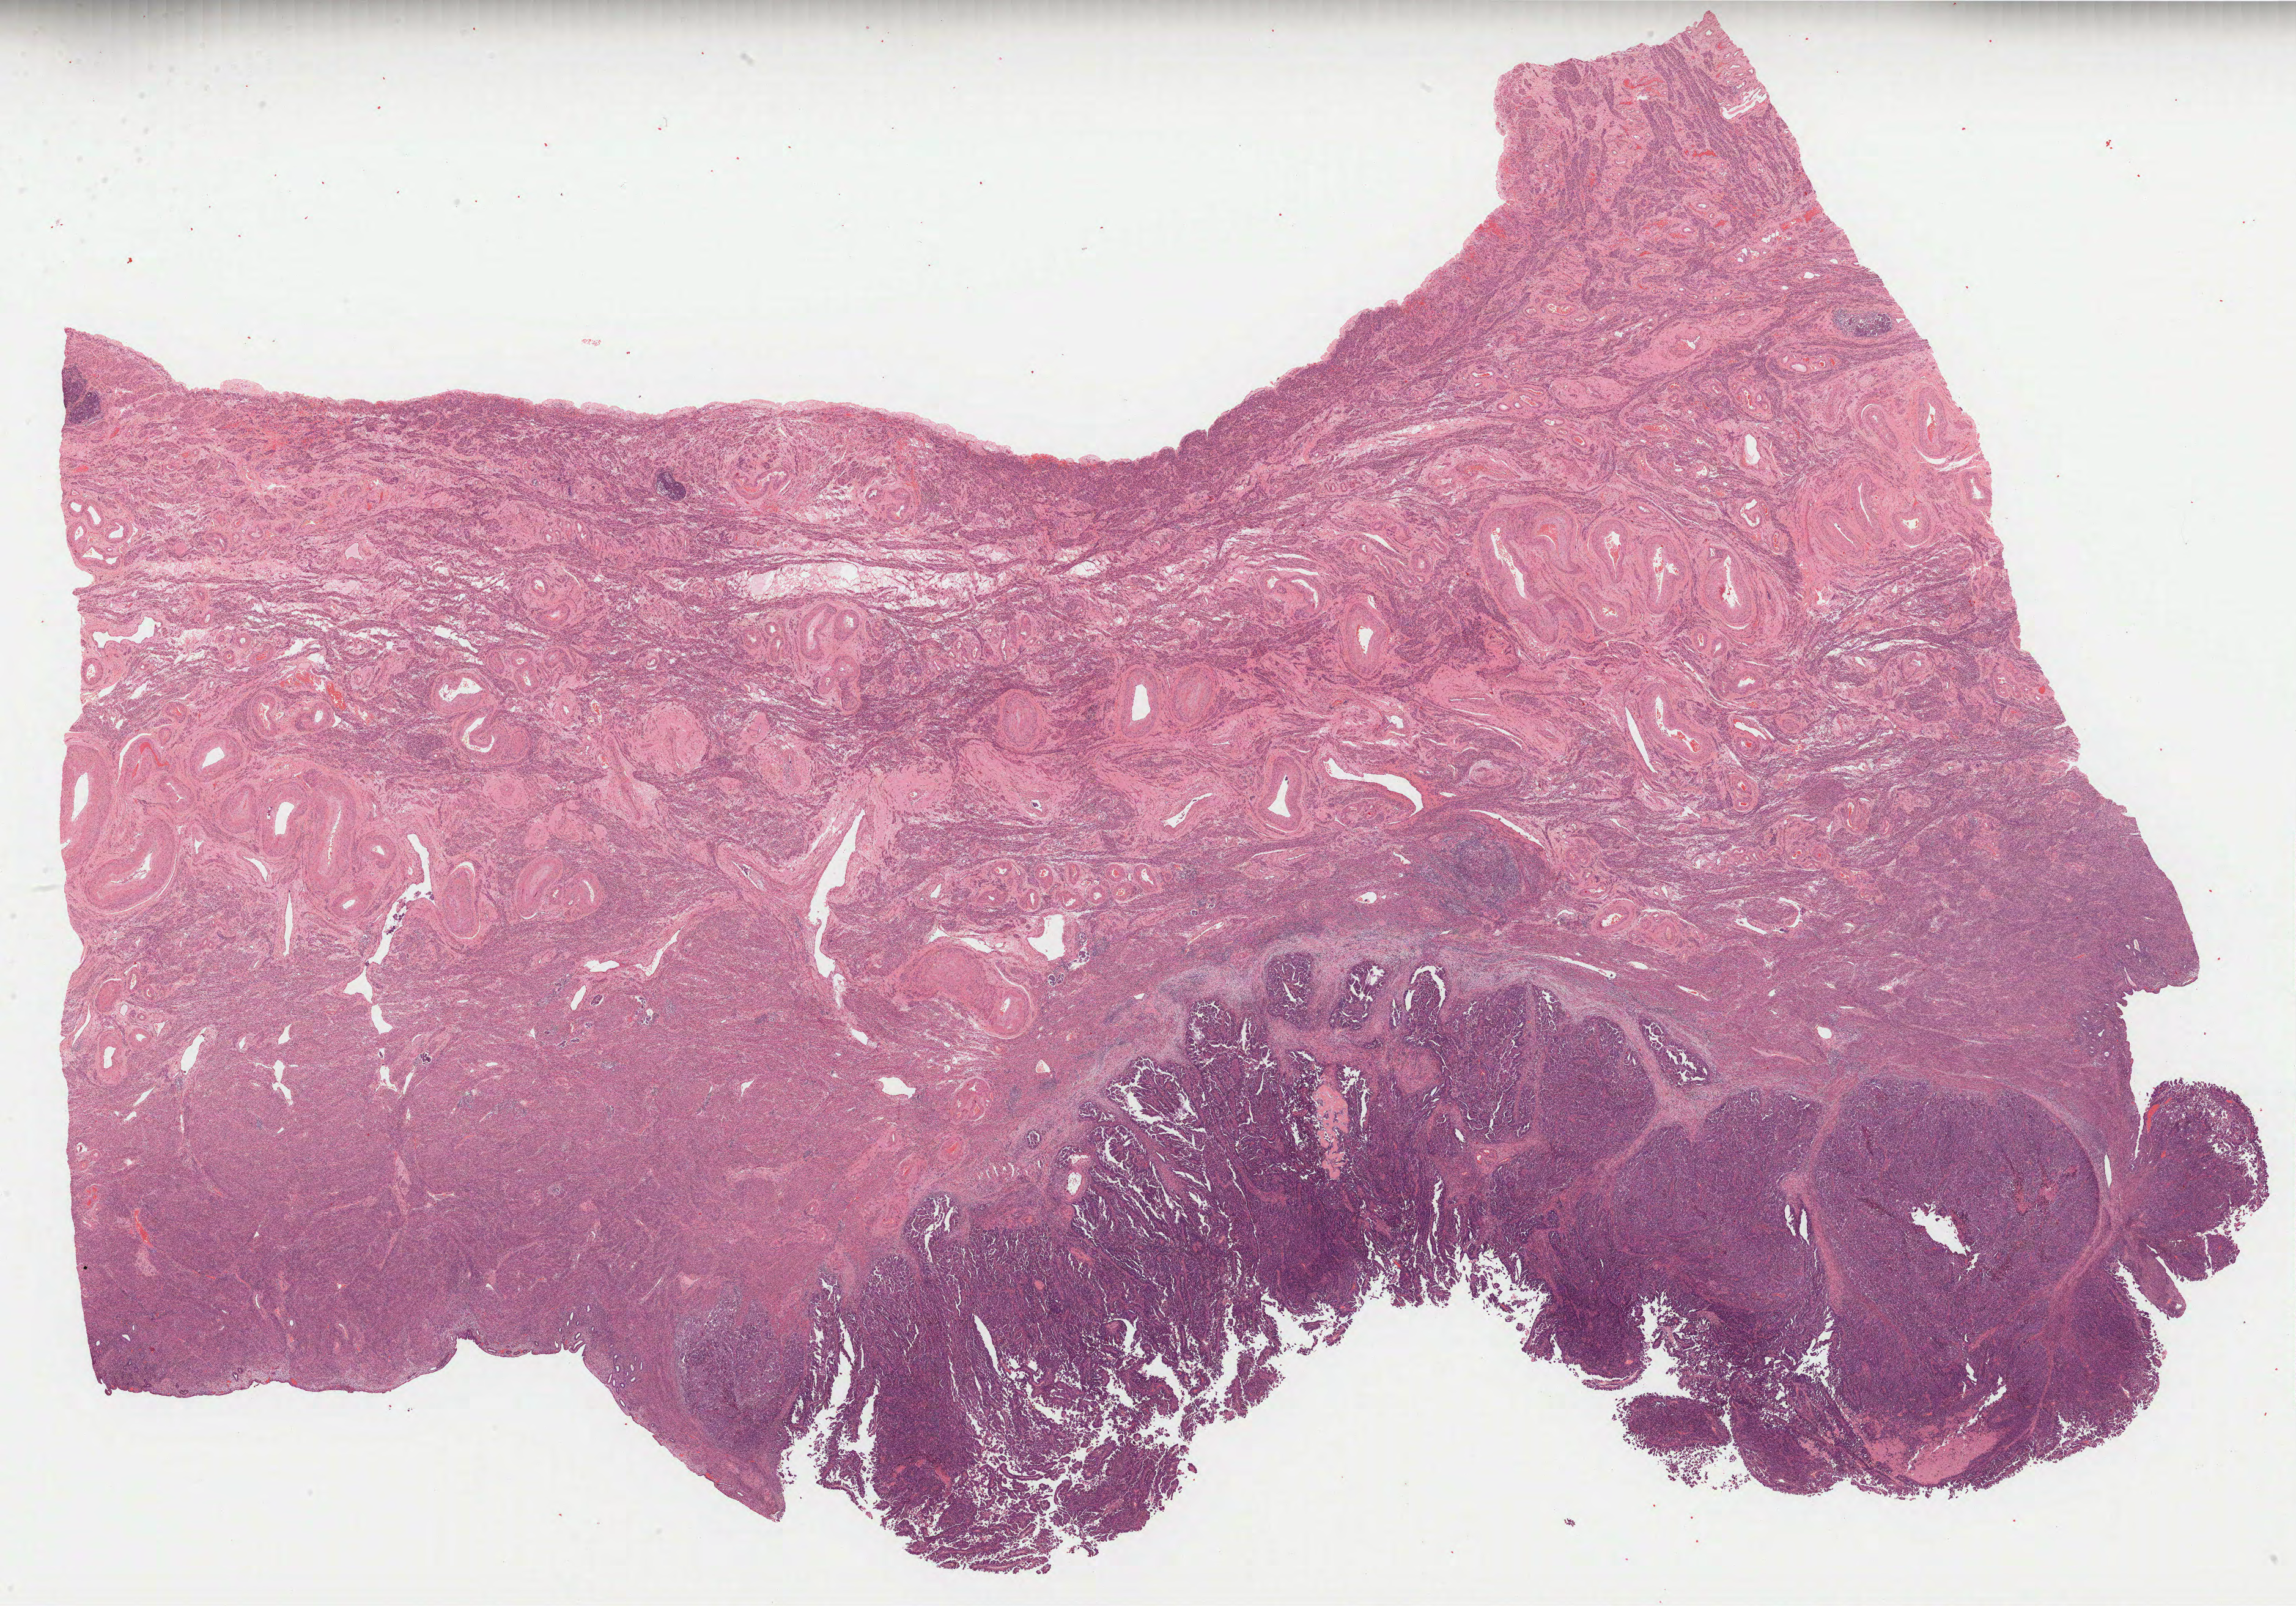
Digitized Hematoxylin and eosin (H&E) stained tissue section (whole slide) — low-resolution overview of the scanned area, about 30.2 x 21.2 mm (slide scanned at 40x); formalin-fixed paraffin-embedded (FFPE) diagnostic section; uterus, primary tumour sample. Female patient; age at initial diagnosis 63 years. Histologic grade: G3 (poorly differentiated).
FIGO stage: IIIC2. Pathologic diagnosis: Serous cystadenocarcinoma, NOS (endometrium).